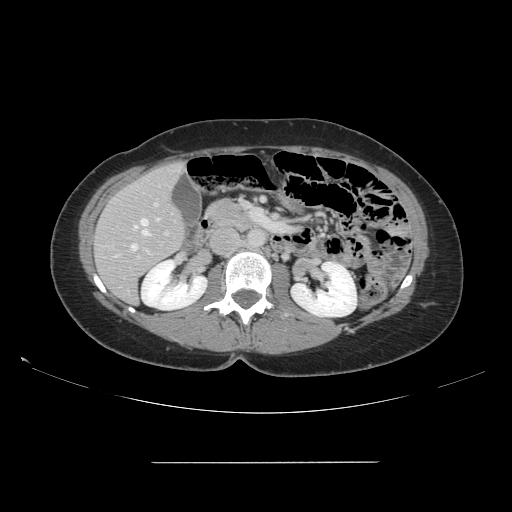
Contrast-enhanced abdominal CT, one axial slice; slice 68 of 151 in the series (ordered by position); soft-tissue window (W 400 / L 40 HU); 2.5 mm slice thickness; 512 × 512 image matrix, field of view 421 × 421 mm. Female patient, age 46 years. Case-level facts recorded for this patient, not image findings: diagnosis: colorectal cancer liver metastases, imaged before liver resection; multiple liver metastases: yes; largest metastasis: 3 cm; disease in both lobes: yes.
Structures marked on this image (manually delineated by an expert):
- hepatic veins: bounding box <131,218,160,251> (left, top, right, bottom; pixels)
- liver: <95,163,185,303>
- planned liver remnant (the part of the liver to remain after resection): <95,164,185,303>
- portal vein (with intrahepatic branches): <137,202,169,259>